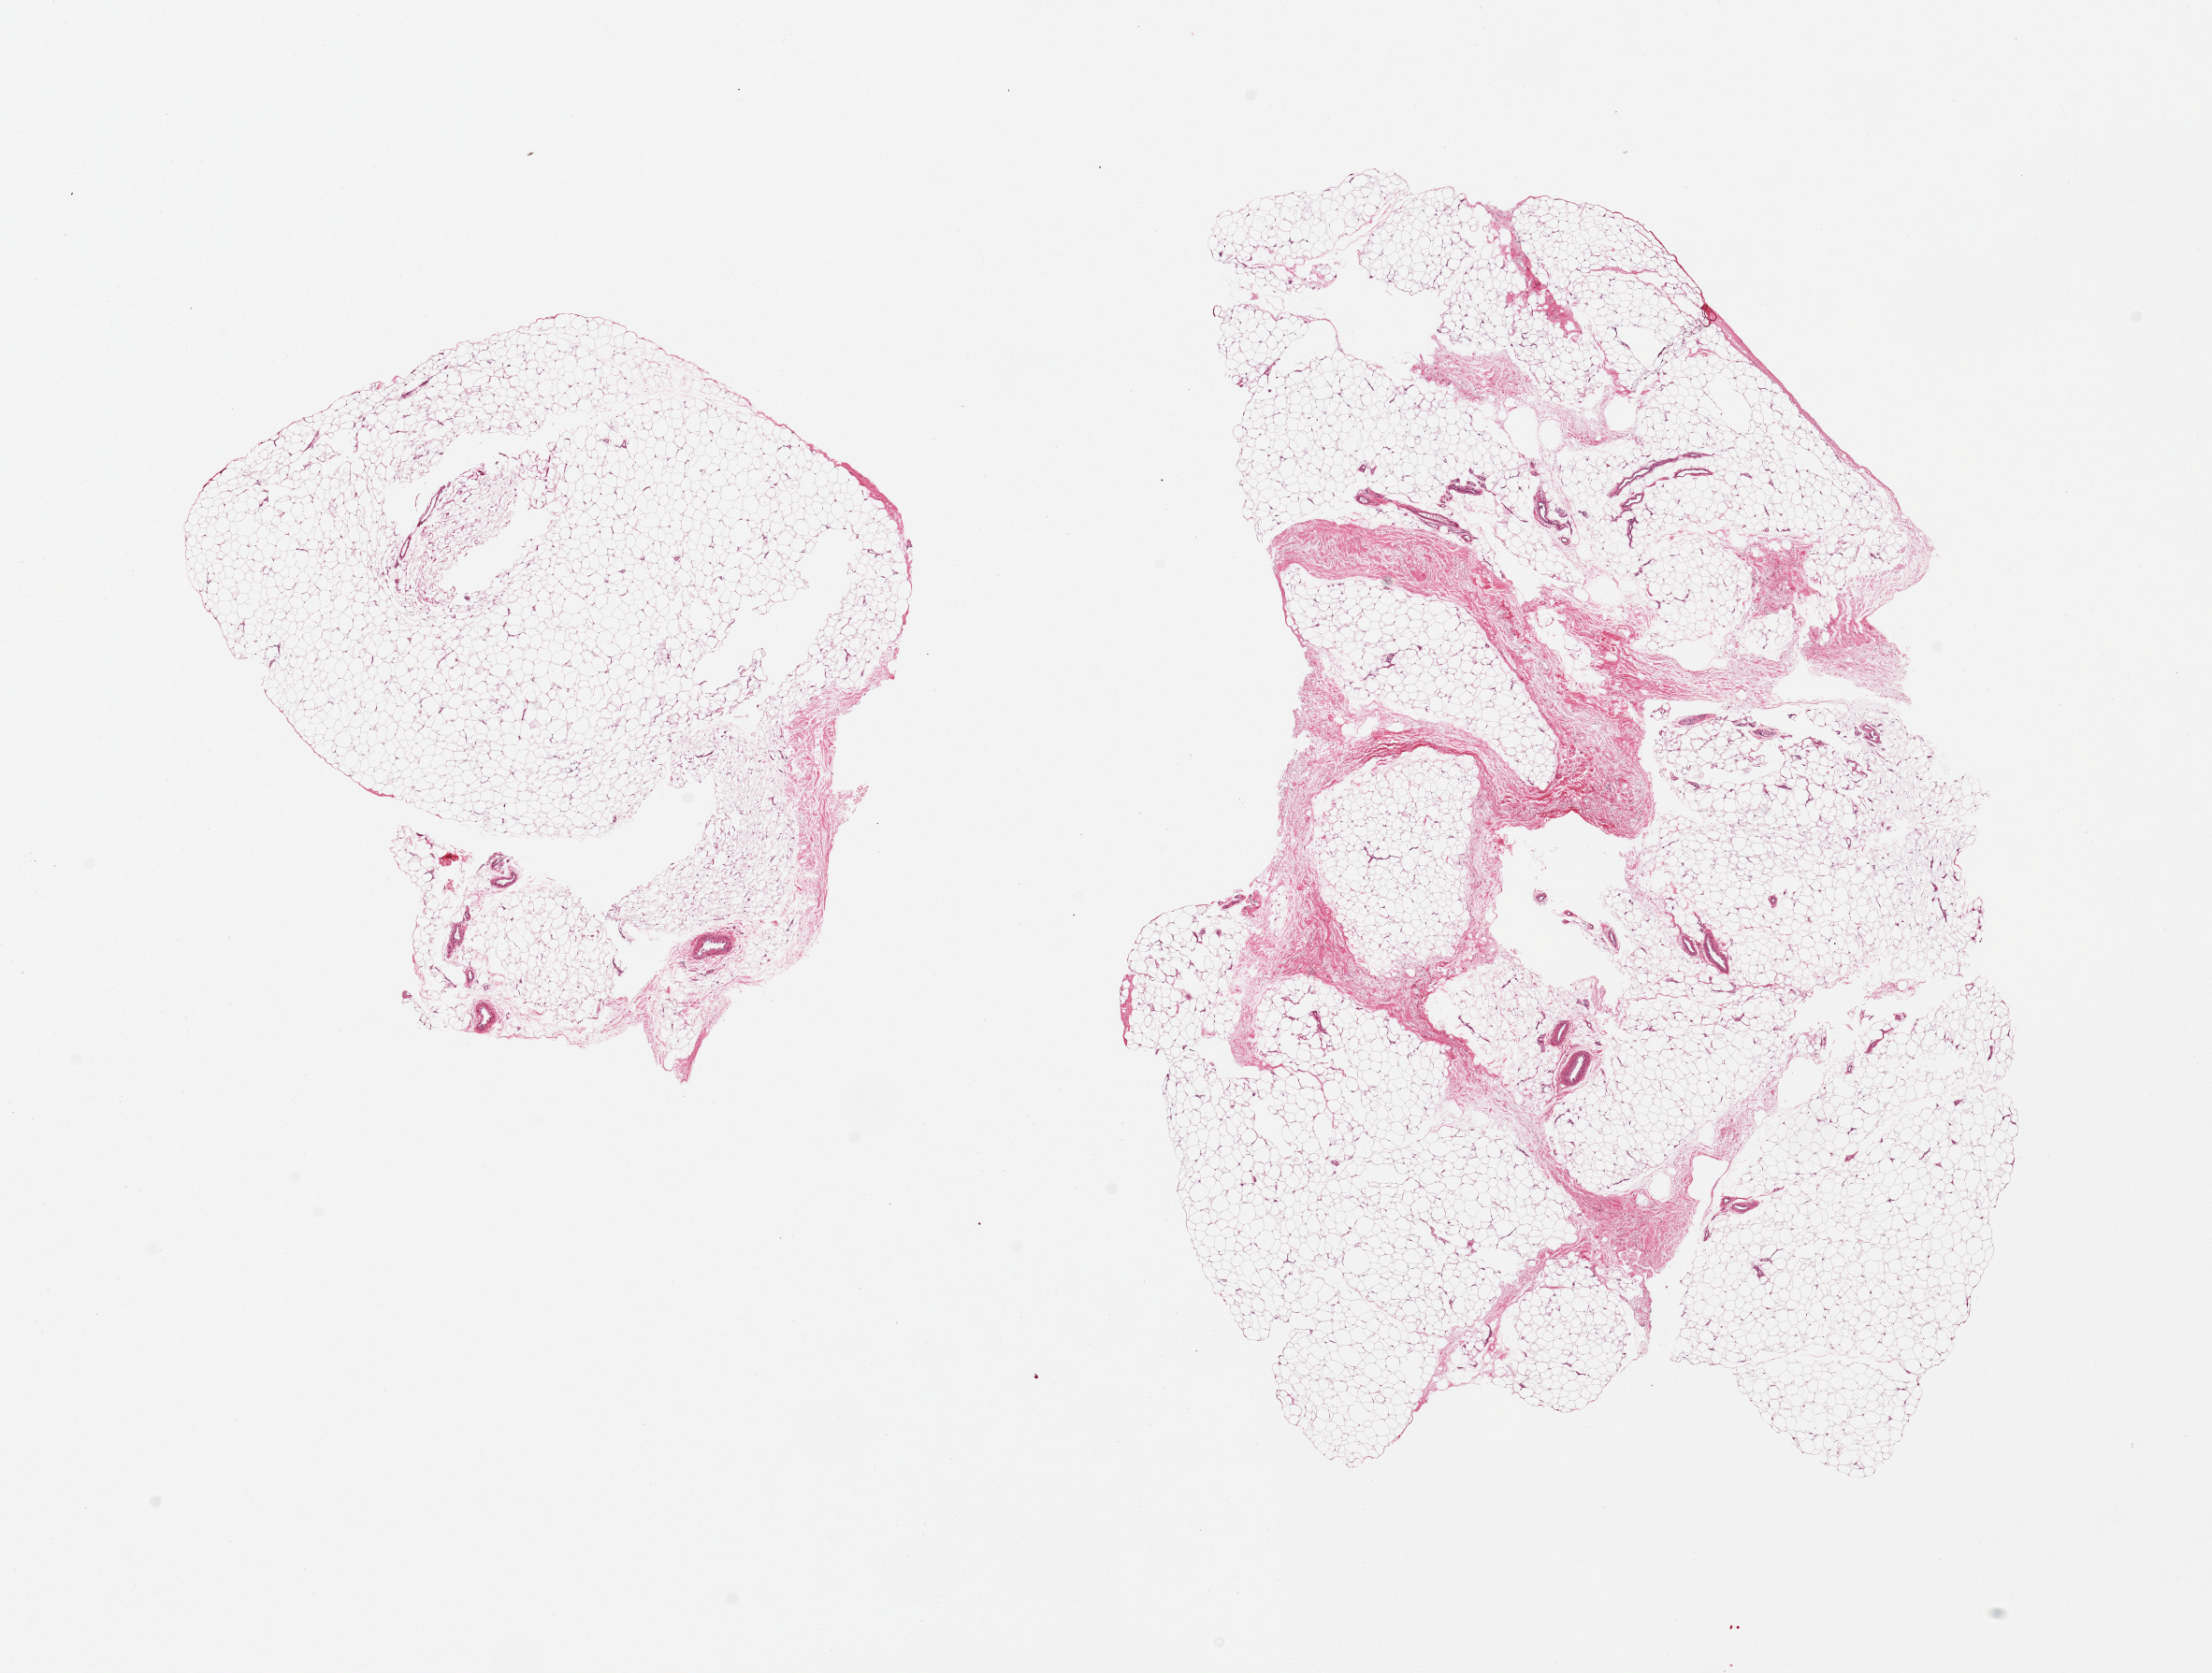
Whole-slide image, H&E stain — a low-resolution overview of the entire scanned area, about 18.7 x 14.1 mm (from a 20x scan). PAXgene-fixed paraffin-embedded (PFPE) section. Sampled site (target tissue): adipose tissue. Donor tissue sample. Donor: female.
- review note (as recorded): 2 pieces